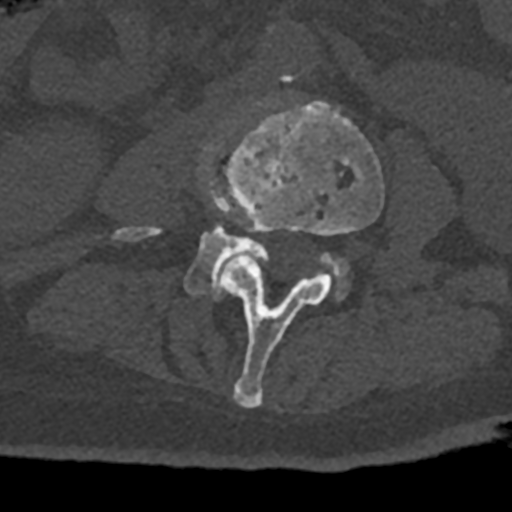
CT including the spine, one axial slice; position 296 of 797 along the scan axis; reconstruction kernel Br40s/3; bone window (W 1800 / L 400 HU); 0.5 mm slice thickness; 512 × 512 image matrix, field of view 160 × 160 mm. Male patient, age 74 years. From the clinical record (not read from this slice): primary cancer: renal; vertebrae with lytic lesions (as recorded): T10, L1, L2, L3, L4, L5.
Annotated regions visible in this slice (semi-automatically segmented with operator editing):
- L3 vertebra: bounding box (x1, y1, x2, y2) in pixels: (221, 101, 384, 408)
- L4 vertebra: (114, 145, 349, 301)